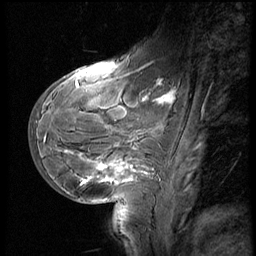
Breast MRI (dynamic contrast-enhanced), one sagittal slice; position 21 of 60 along the scan axis; 3 images stored at this slice position (order not interpretable as contrast timing); 1.5 T; TE 4.2 ms, TR 8.9 ms; 2.5 mm slice thickness; 256 × 256 image matrix, field of view 200 × 200 mm. Female patient, age 29 years. Case-level facts recorded for this patient, not image findings: setting: breast cancer imaged before/during neoadjuvant chemotherapy.
Structures marked on this image (semi-automatically segmented with operator editing):
- analysis volume of interest (the breast-tissue region the enhancement analysis was run in; not a lesion): bounding box <30,57,185,200> (left, top, right, bottom; pixels)
- tumour enhancement mask (voxels above the 140 % enhancement threshold inside the analysis volume of interest): <78,87,172,186>